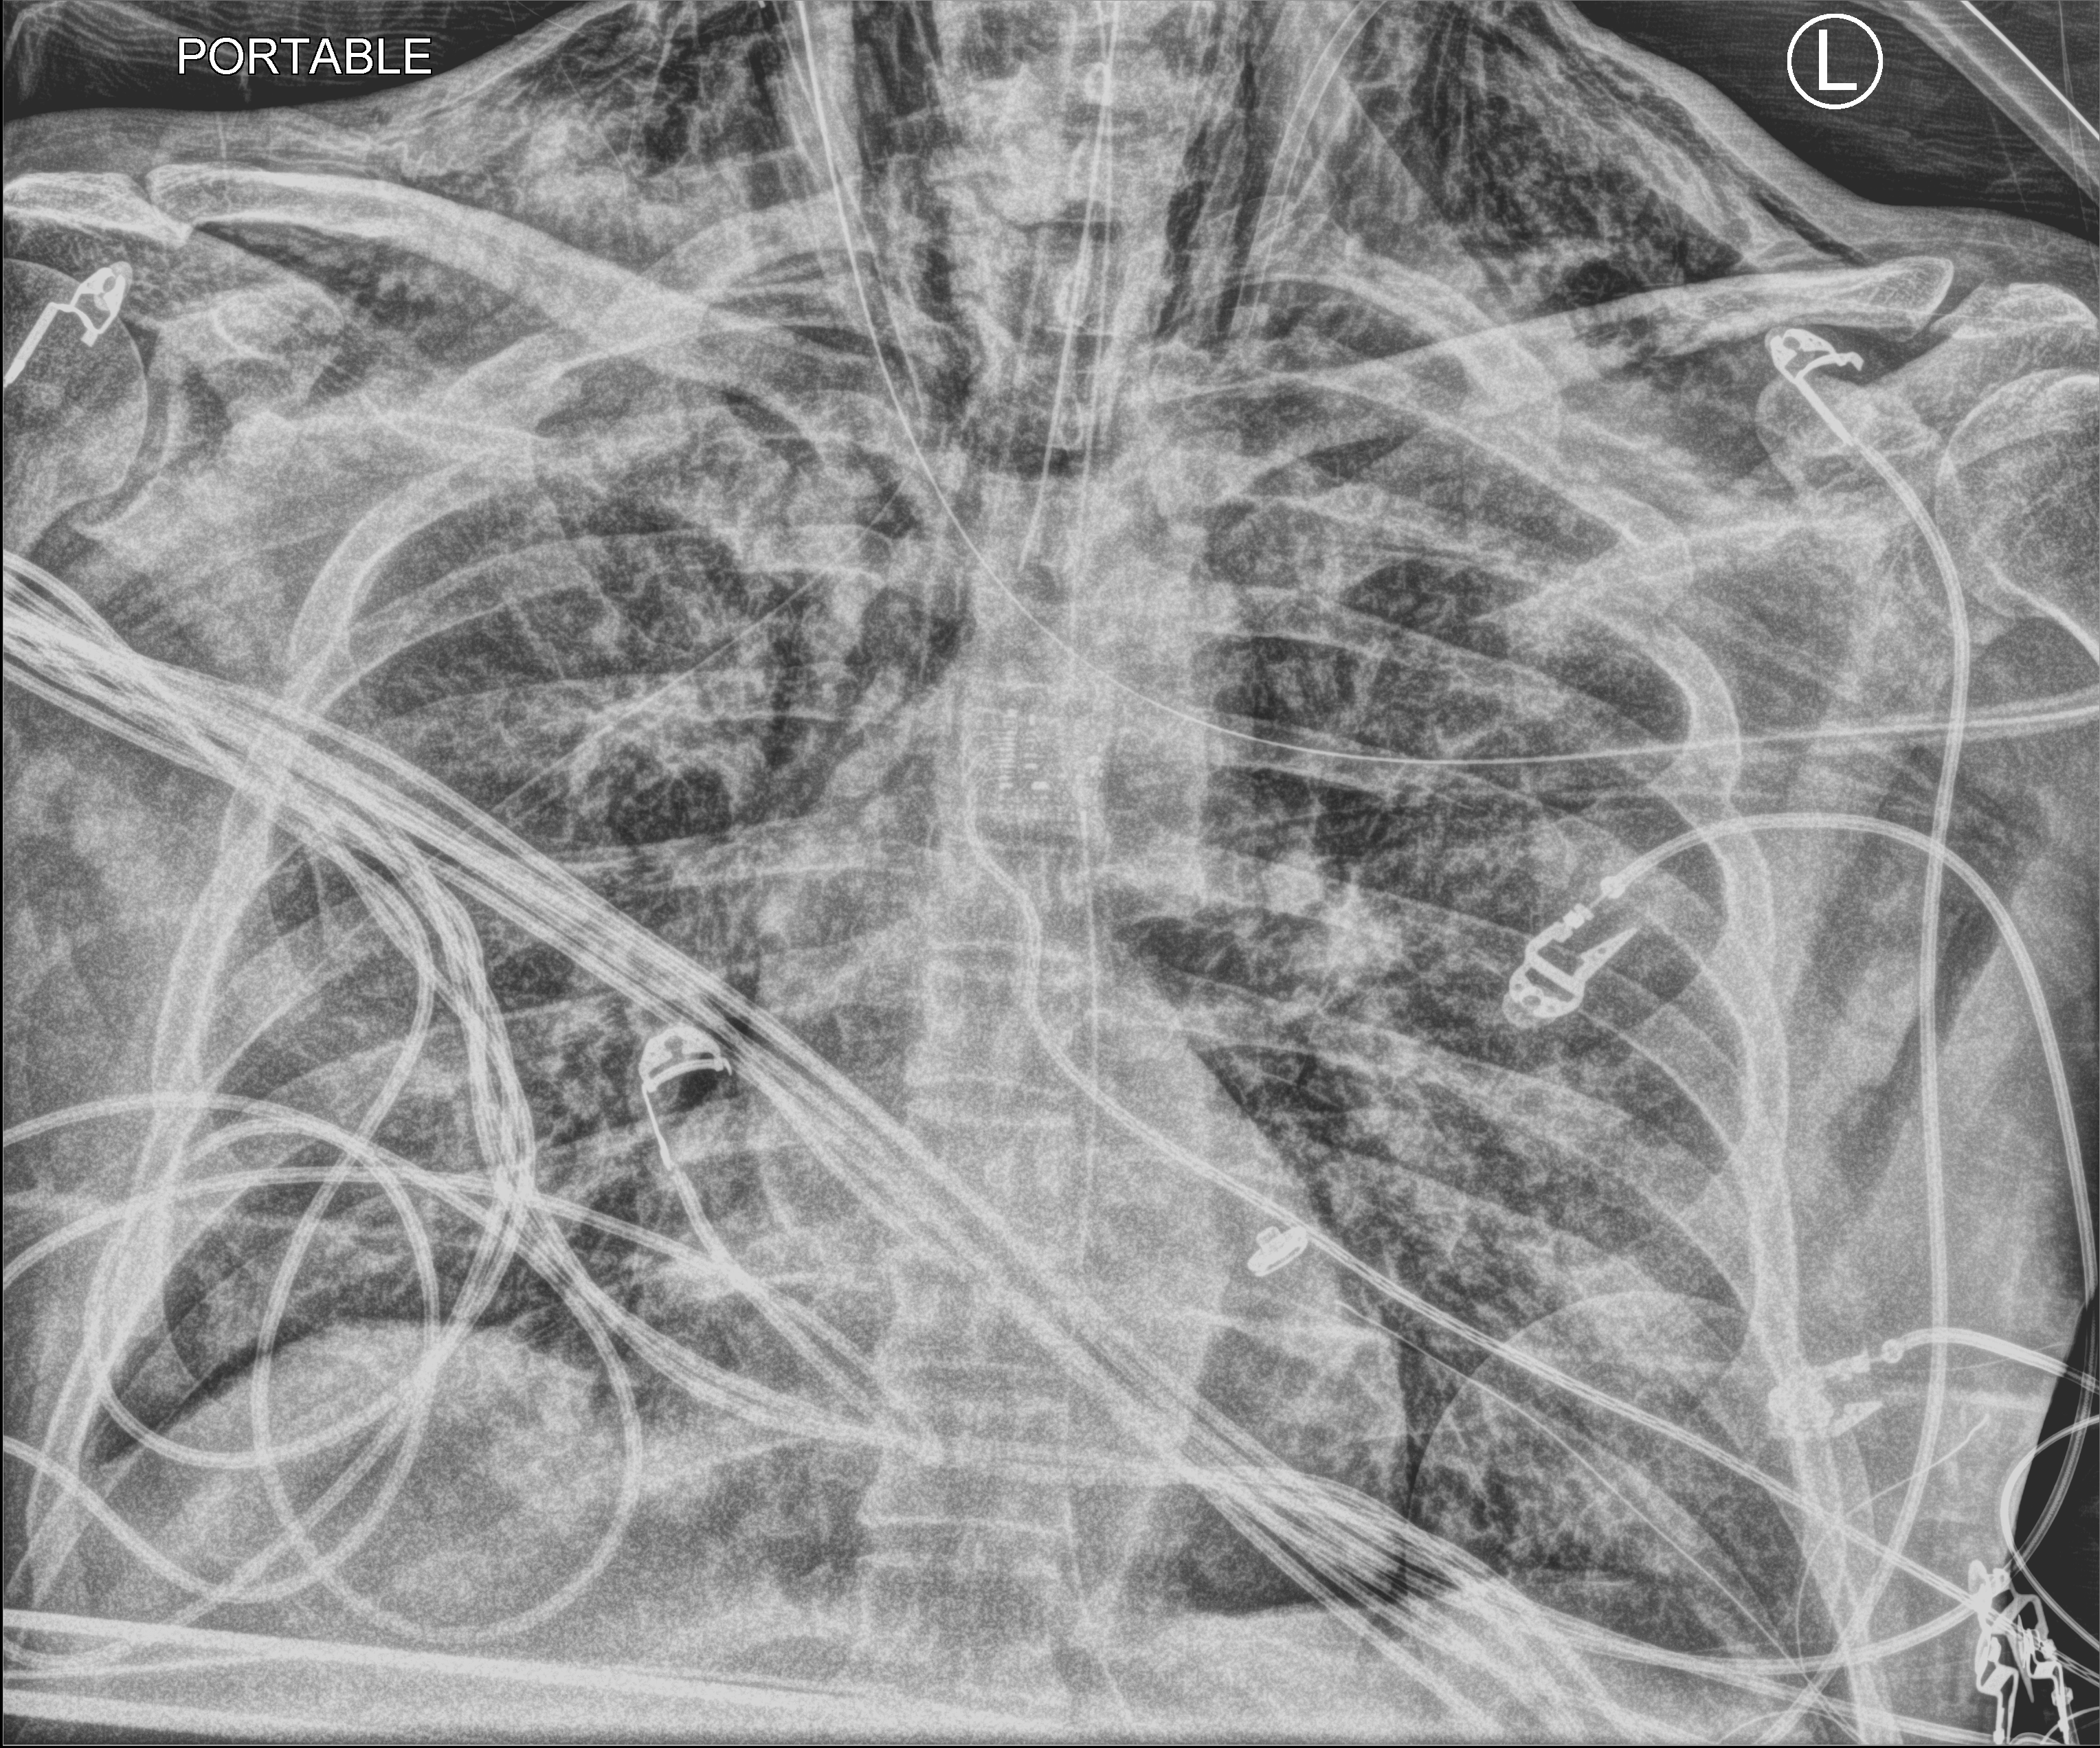
Portable chest radiograph, anteroposterior (AP) projection. Patient hospitalised with COVID-19; male, aged 60–74 years.
From the hospital-stay record, not from the radiograph (when in the stay this image was taken is not recorded): diabetes (admission record): no; admitted to intensive care during this hospital stay: yes; chronic kidney disease (admission record): no.